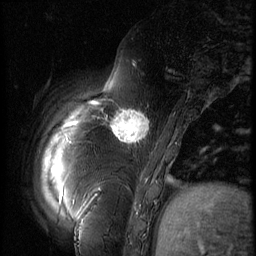
Breast MRI (dynamic contrast-enhanced), one sagittal slice. Position 12 of 60 along the scan axis. 3 images stored at this slice position (order not interpretable as contrast timing). 1.5 T. TE 4.2 ms, TR 9 ms. 2.5 mm slice thickness. 256 × 256 image matrix. Female patient, age 57 years. Case-level facts recorded for this patient, not image findings: setting: breast cancer imaged before/during neoadjuvant chemotherapy; receptor status: triple-negative.
Structures marked on this image (semi-automatically segmented with operator editing):
- analysis volume of interest (the breast-tissue region the enhancement analysis was run in; not a lesion): bounding box <106,101,157,152> (left, top, right, bottom; pixels)
- tumour enhancement mask (voxels above the 140 % enhancement threshold inside the analysis volume of interest): <111,109,150,144>